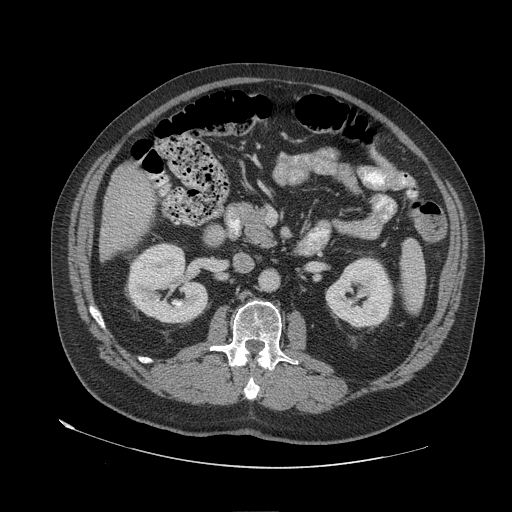
Contrast-enhanced abdominal CT (liver protocol), one axial slice; position 18 of 79 along the scan axis; reconstruction kernel STANDARD; 140 kVp; soft-tissue window (W 400 / L 40 HU); 2.5 mm slice thickness; 512 × 512 image matrix, field of view 480 × 480 mm. From the clinical record (not read from this slice): diagnosis: hepatocellular carcinoma (patient treated with transarterial chemoembolisation; whether this scan precedes or follows treatment is not stated here); TNM stage (as recorded): Stage-IVA; Child-Pugh class: A; tumour differentiation: well differentiated.
Outlined on this slice (semi-automatically segmented with operator editing):
- liver parenchyma outside the tumour (the mass and vessels are separate outlines, so this box may not span the whole liver): bounding box <100,164,156,258> (left, top, right, bottom; pixels)